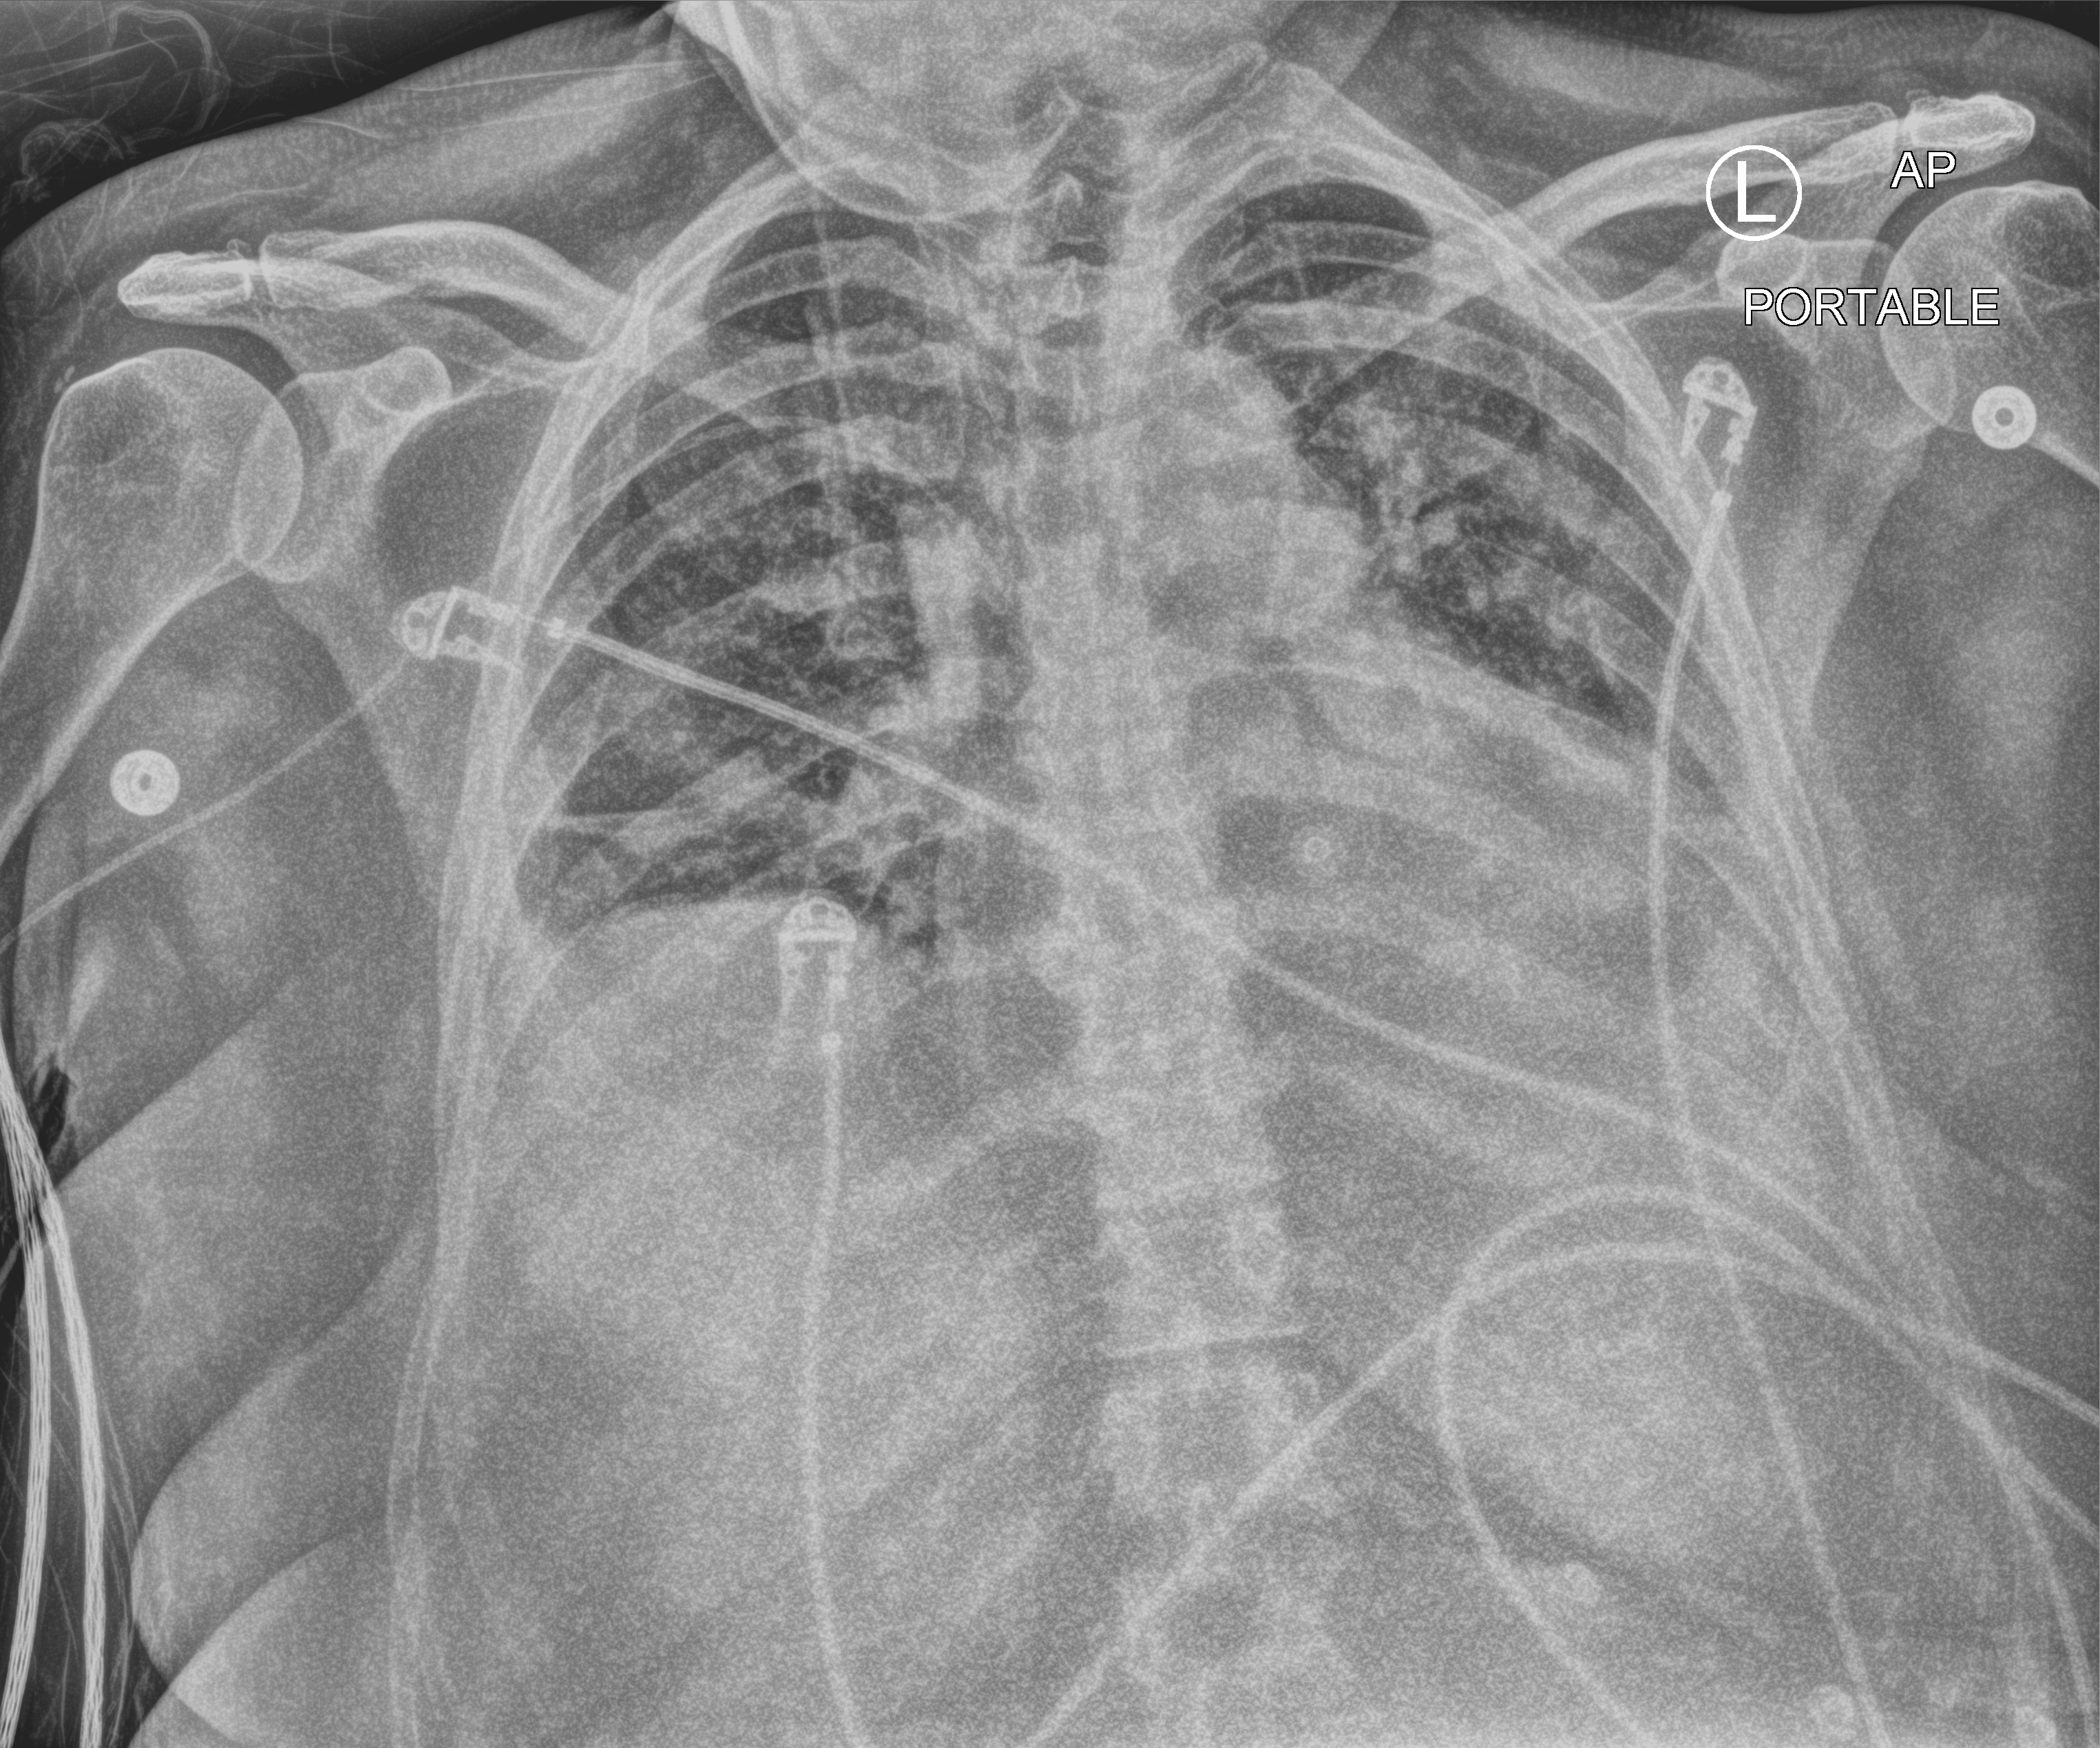
Bedside chest radiograph (computed radiography); anteroposterior (AP) projection. Patient hospitalised with COVID-19; female, aged 60–74 years.
From the hospital-stay record, not from the radiograph (when in the stay this image was taken is not recorded):
- length of hospital stay: 50 days
- admitted to intensive care during this hospital stay: yes